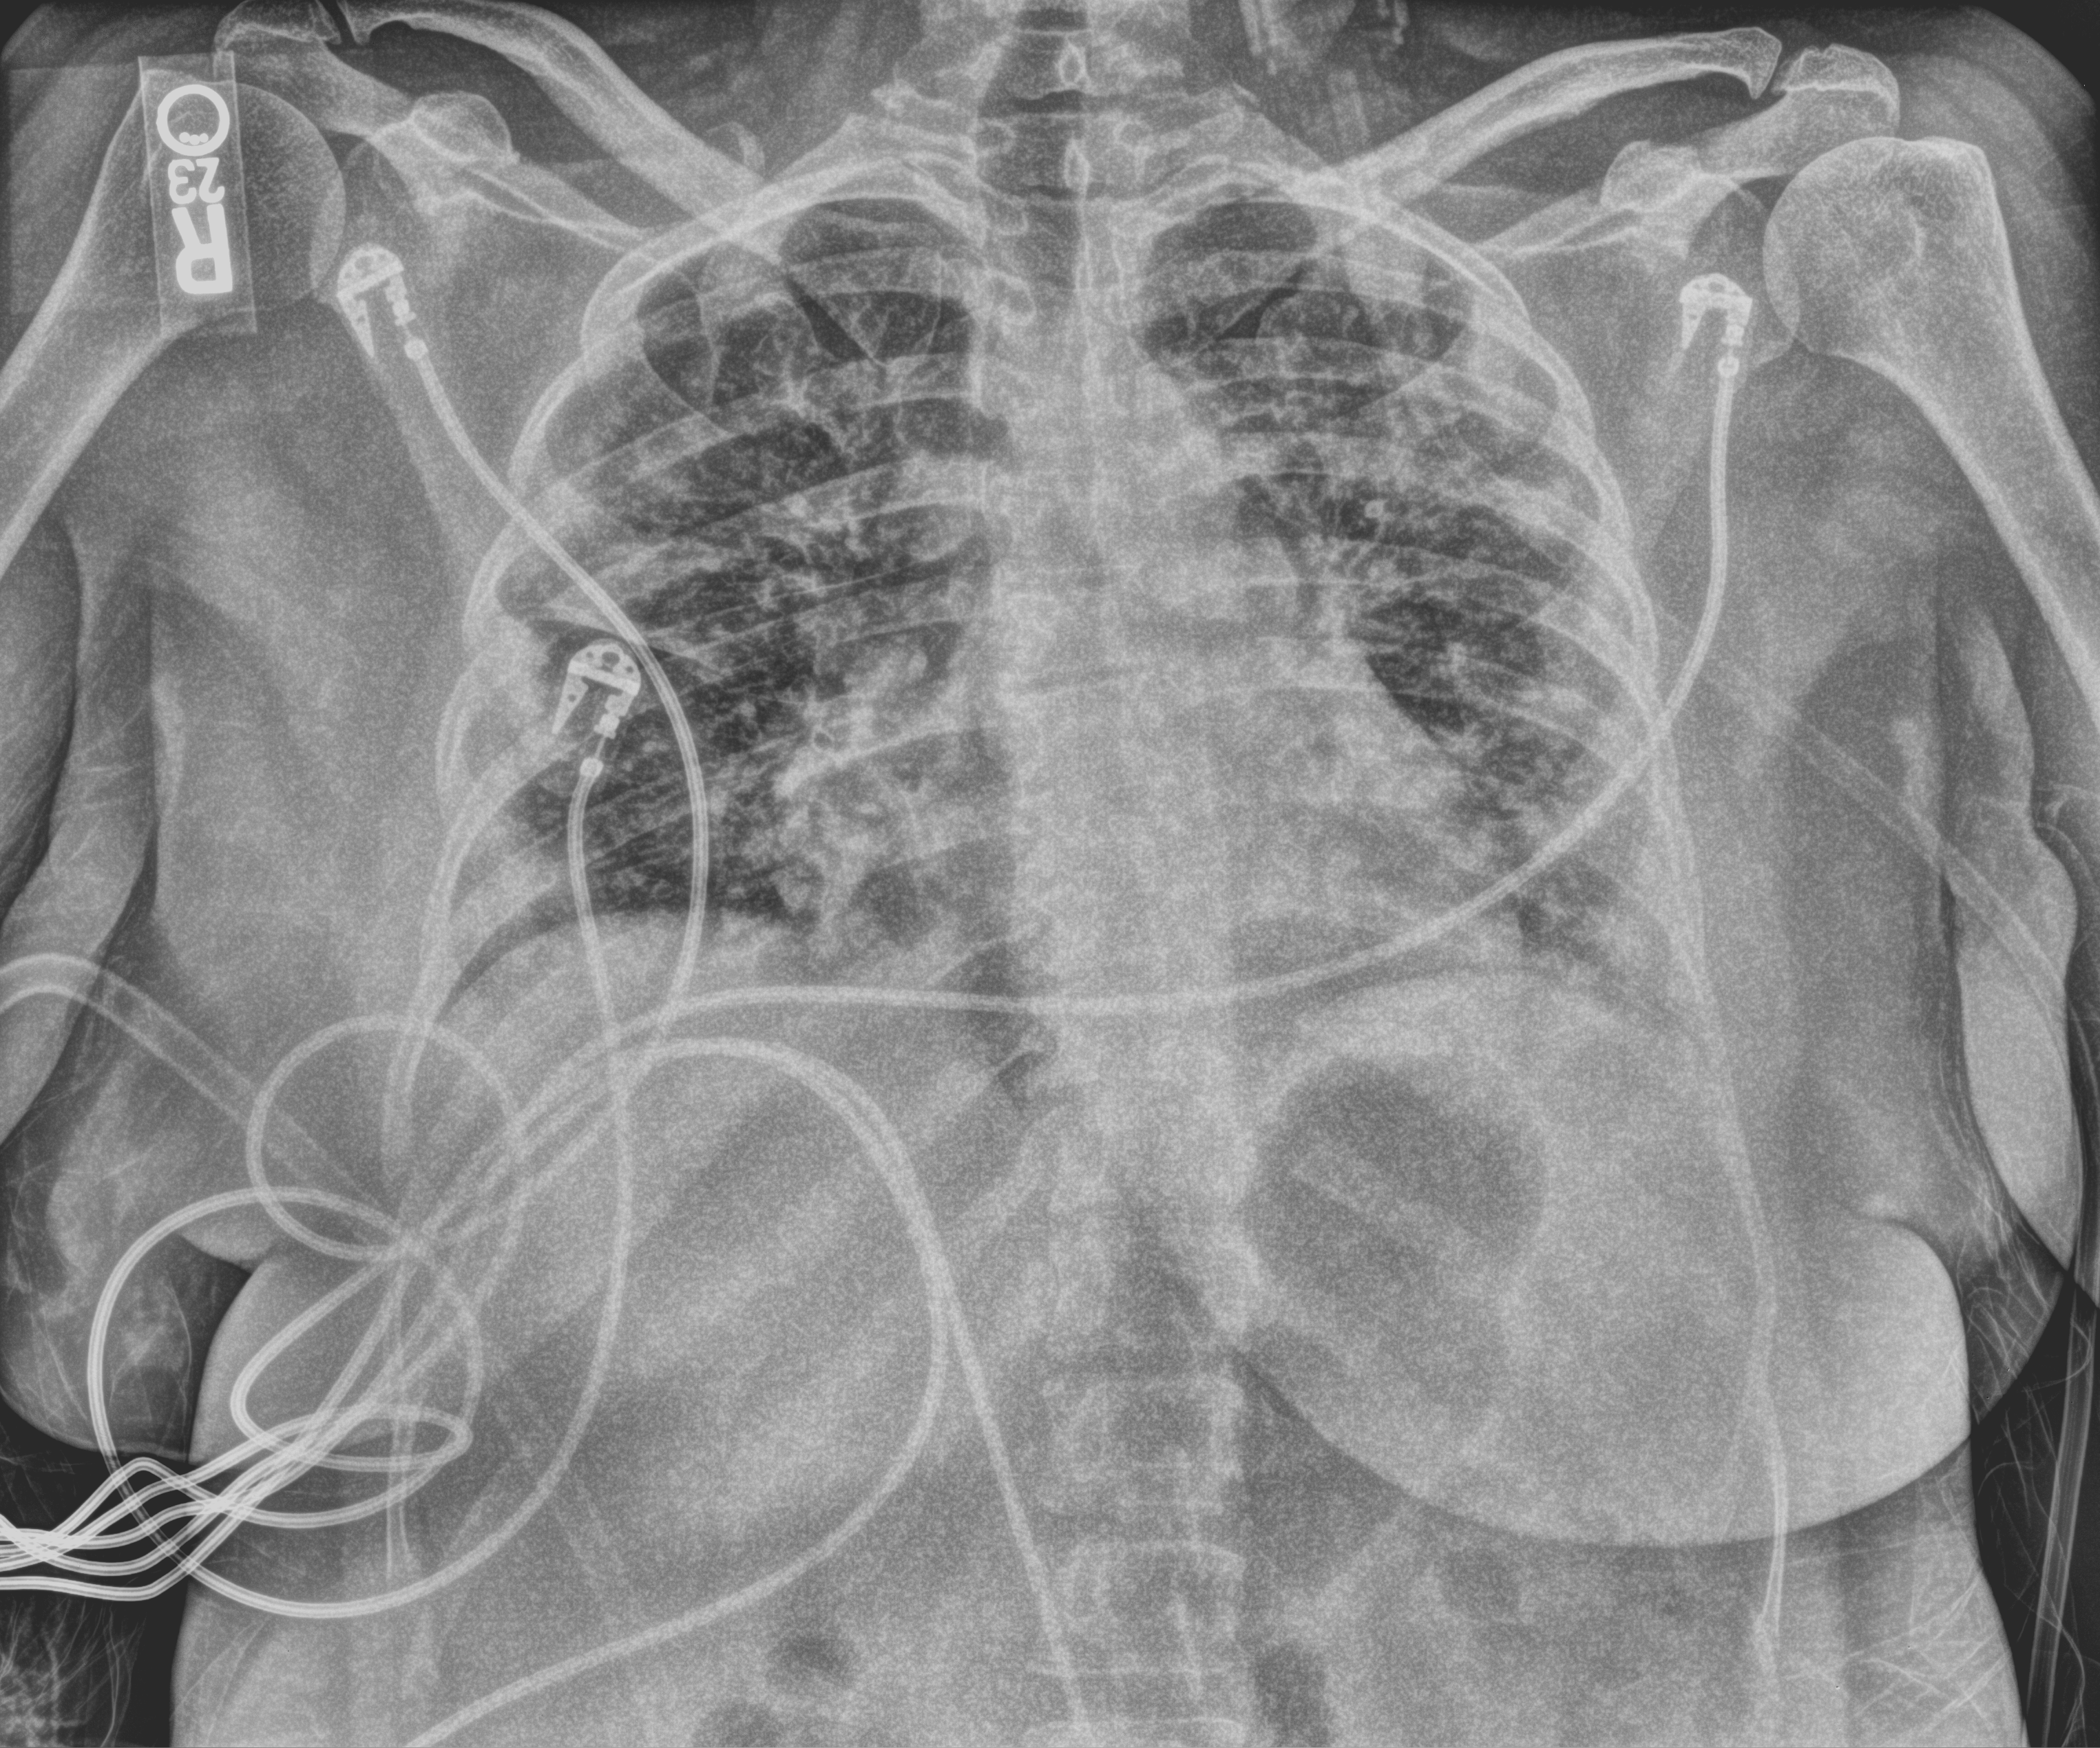
Chest X-ray (portable); anteroposterior (AP) projection. Female patient hospitalised with COVID-19, age 18–59 years.
Admission-level facts for this patient (not findings on this image; timing relative to this image not recorded):
- length of hospital stay: 14 days
- admitted to intensive care during this hospital stay: no
- mechanically ventilated during this hospital stay: no